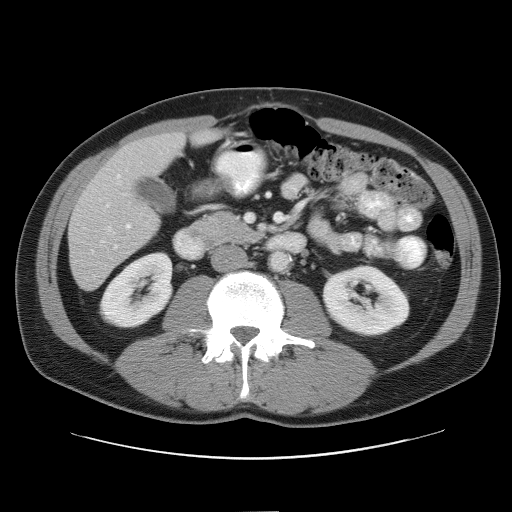
Contrast-enhanced abdominal CT, one axial slice. Slice 22 of 52 in the series (ordered by position). 120 kVp. Soft-tissue window (W 400 / L 40 HU). 5 mm slice thickness. 512 × 512 image matrix. Male patient, age 70 years. From the clinical record (not read from this slice): diagnosis: colorectal cancer liver metastases, imaged before liver resection; multiple liver metastases: yes; largest metastasis: 4 cm; disease in both lobes: yes.
Annotated regions visible in this slice (expert manual segmentation):
- hepatic veins: box from (x=77, y=209) to (x=118, y=254) px
- liver: (x=70, y=132)–(x=217, y=289)
- planned liver remnant (the part of the liver to remain after resection): (x=118, y=132)–(x=216, y=177)
- portal vein (with intrahepatic branches): (x=106, y=174)–(x=131, y=229)